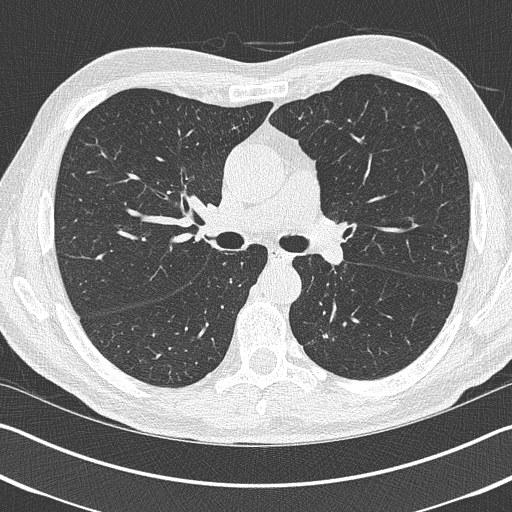
Low-dose screening chest CT, one axial slice. Position 250 of 402 along the scan axis. Lung window (W 1500 / L -600 HU). 1 mm slice thickness. 512 × 512 image matrix, field of view 340 × 340 mm.
Structures marked on this image (manually delineated by an expert):
- lesion 1 (tumor, lower lobe of left lung): box from (x=323, y=334) to (x=328, y=338) px